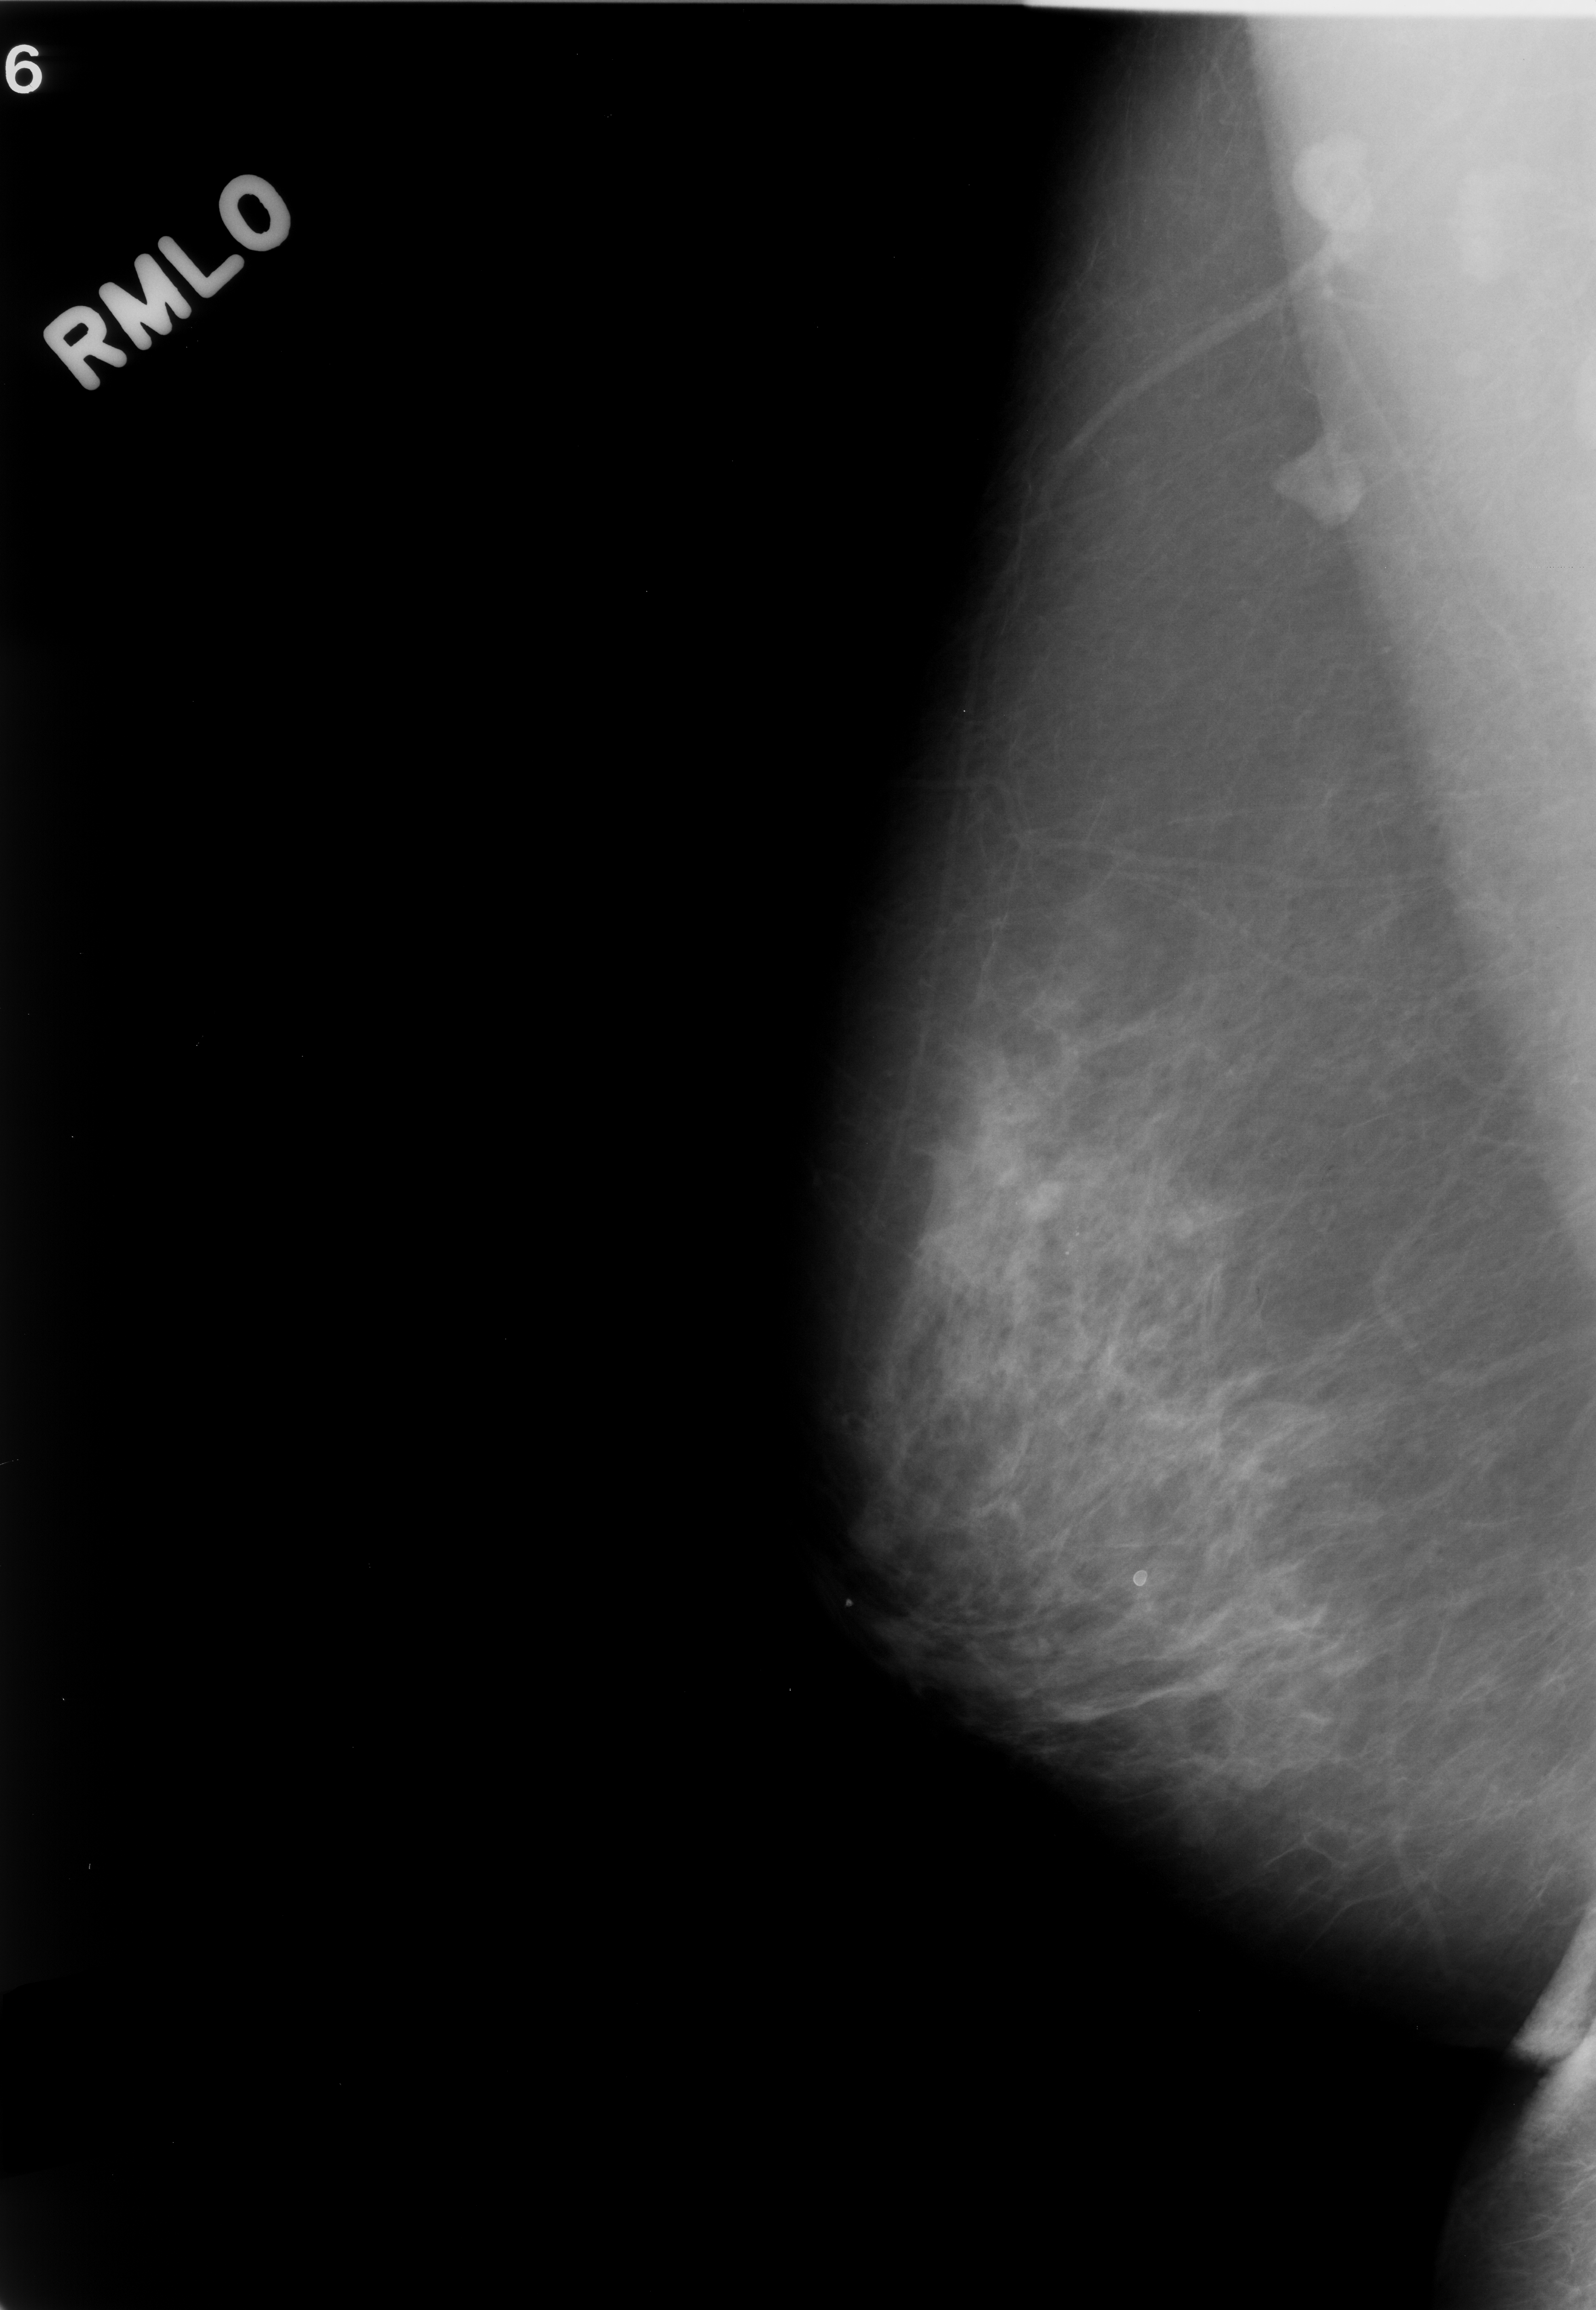
Scanned film-screen mammogram. Right breast. MLO view. Breast composition: scattered fibroglandular densities (BI-RADS density category 2 of 4). 1596 × 2310 image matrix.
Expert-marked regions of interest on this image (one box per marked abnormality):
- calcifications, morphology pleomorphic, distribution clustered; BI-RADS assessment category 3; pathology result (as recorded, not read from the image): benign: bounding box <985,1156,1116,1309> (left, top, right, bottom; pixels)